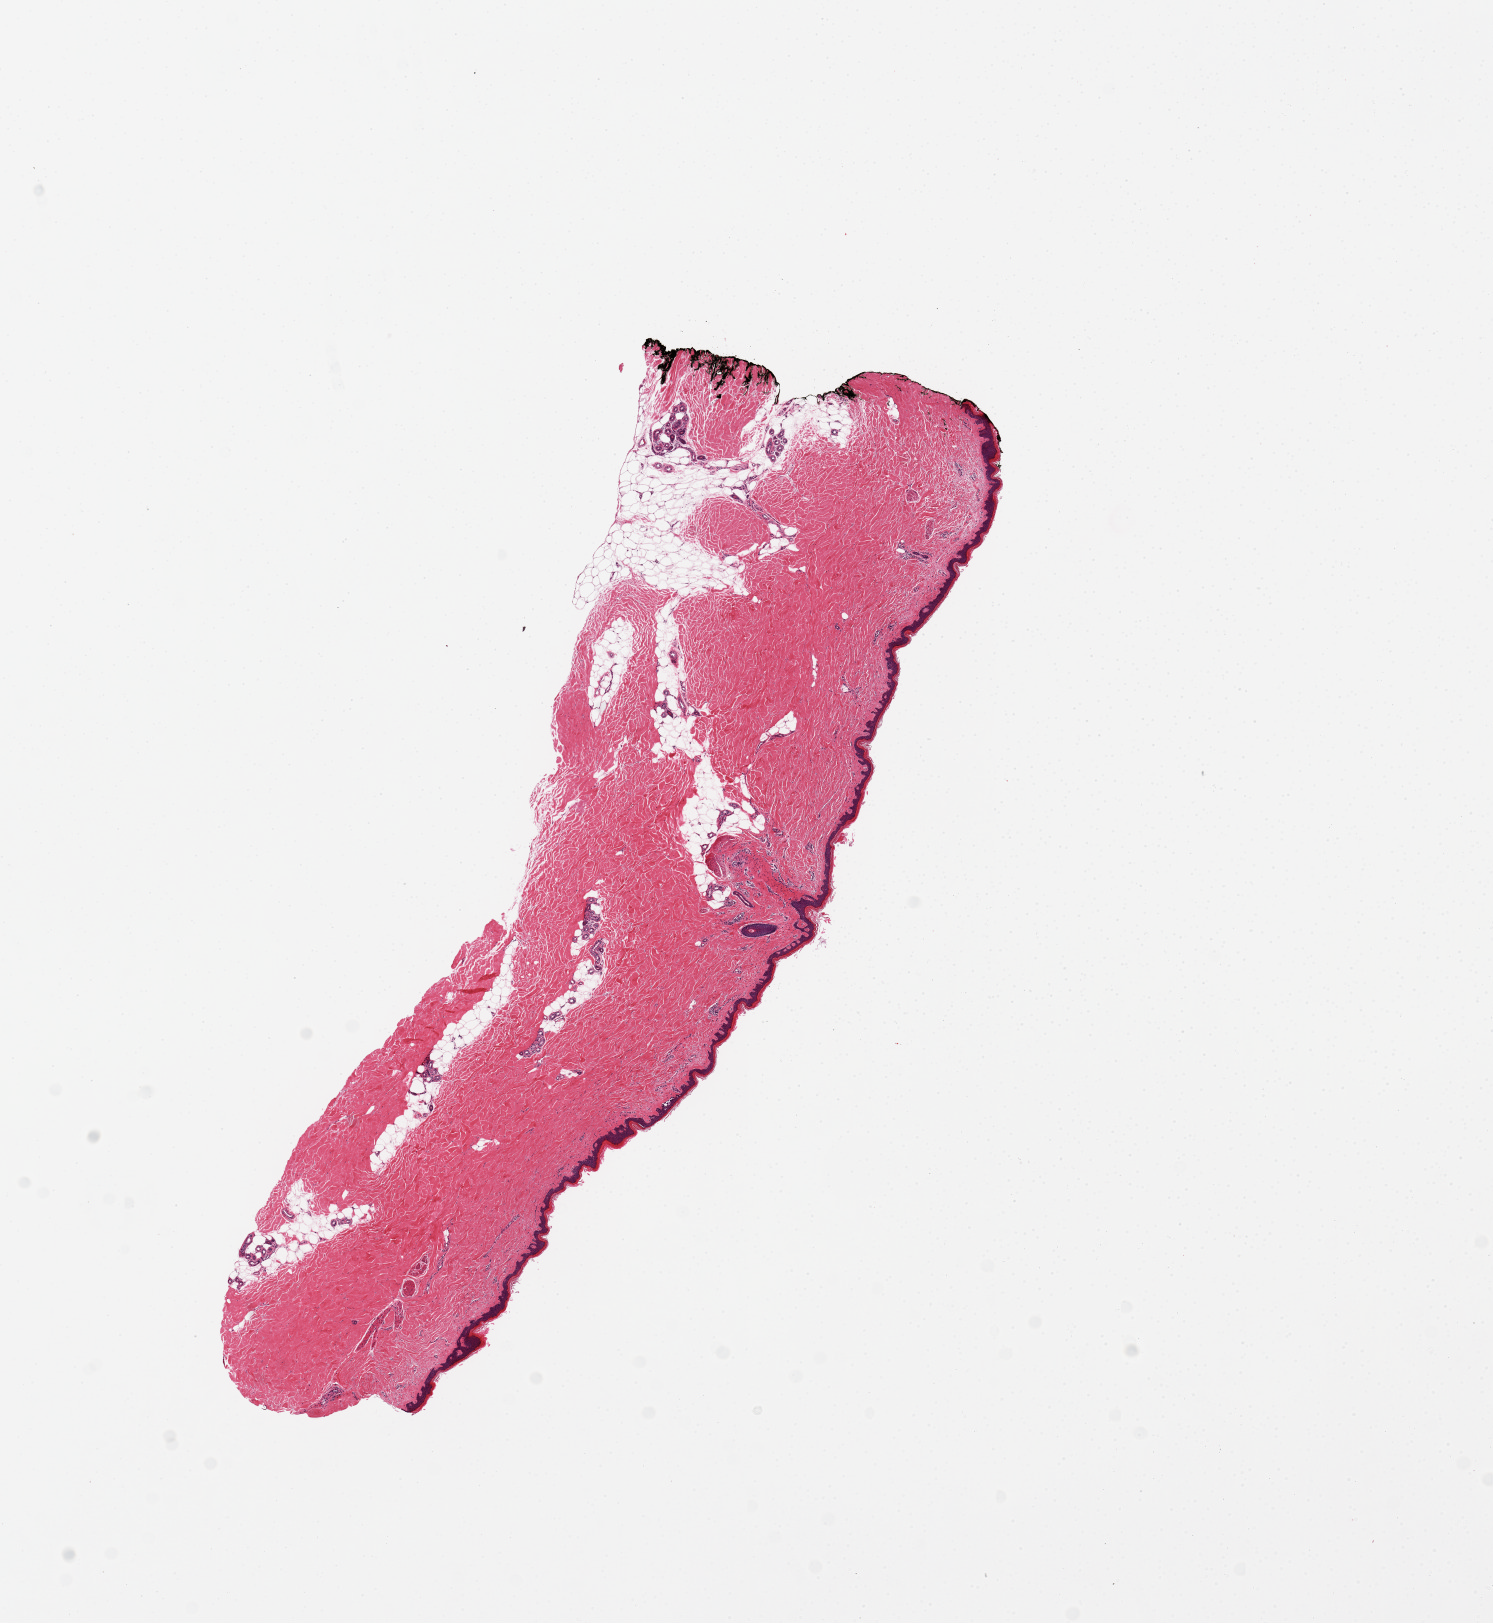
Digitized haematoxylin and eosin-stained section — low-resolution overview of the scanned area, about 11.8 x 12.8 mm (acquisition: 20x scan); PAXgene-fixed, paraffin-embedded tissue; sampled site (target tissue): skin of lower leg; donor tissue sample. Donor: male.
• review note (as recorded): 1 piece; well trimmed, comparable to 25 block